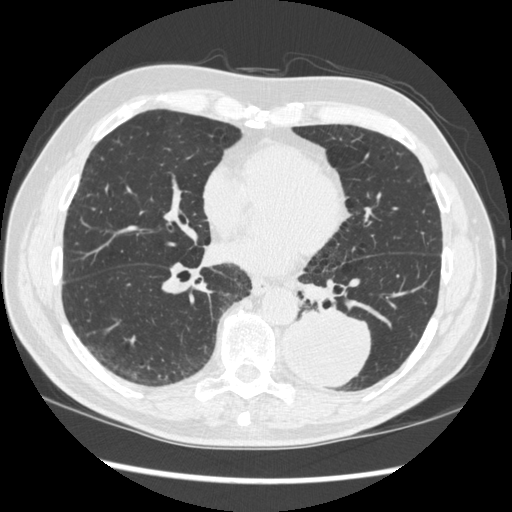
Low-dose screening chest CT, axial slice; baseline annual screen; lung window (W 1500 / L -600 HU); 1.25 mm slice thickness; standard (soft-tissue) reconstruction kernel (STANDARD). Male, age 72 years at enrolment. Current smoker at enrolment.
Expert reader's lesion annotation, bounding box [x1, y1, x2, y2] px = [269, 300, 373, 390]. The screening reader recorded 2 non-calcified nodules or masses ≥4 mm on this exam (left lower lobe, right middle lobe); which of them this box marks is not recorded. Official screen result: positive, change unspecified: nodule(s) >= 4 mm or enlarging nodule(s), mass(es), or other non-specific abnormalities suspicious for lung cancer. Lung cancer was diagnosed 37 days after this screen: squamous cell carcinoma, NOS, left lower lobe, stage IIIA (AJCC 6th edition), 60 mm at pathology.